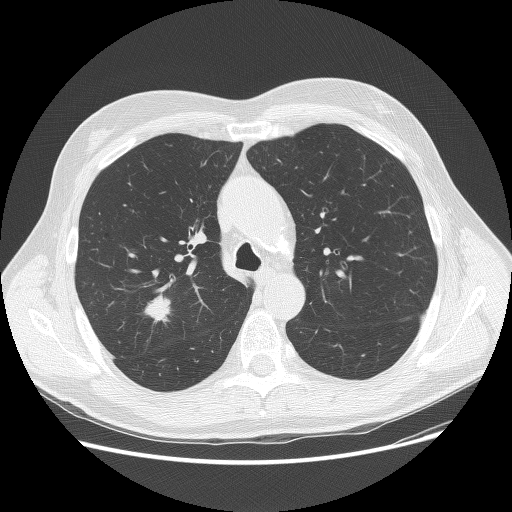
Axial slice from a low-dose chest CT screening exam; first (baseline) screen; lung window (W 1500 / L -600 HU); lung (sharp) reconstruction kernel (BONE); 120 kVp; slice 50 of 156 in the series. Male participant, aged 70 years at enrolment. Current smoker at enrolment.
Expert reader's lesion annotation, bounding box <131,282,193,337> (left, top, right, bottom; pixels). The screening reader recorded 2 non-calcified nodules or masses ≥4 mm on this exam (right upper lobe, left lower lobe); which of them this box marks is not recorded. Official screen result: positive, change unspecified: nodule(s) >= 4 mm or enlarging nodule(s), mass(es), or other non-specific abnormalities suspicious for lung cancer. Lung cancer was diagnosed 15 days after this screen: adenocarcinoma, NOS, right upper lobe, poorly differentiated (G3), stage IIA (AJCC 6th edition), 23 mm at pathology.